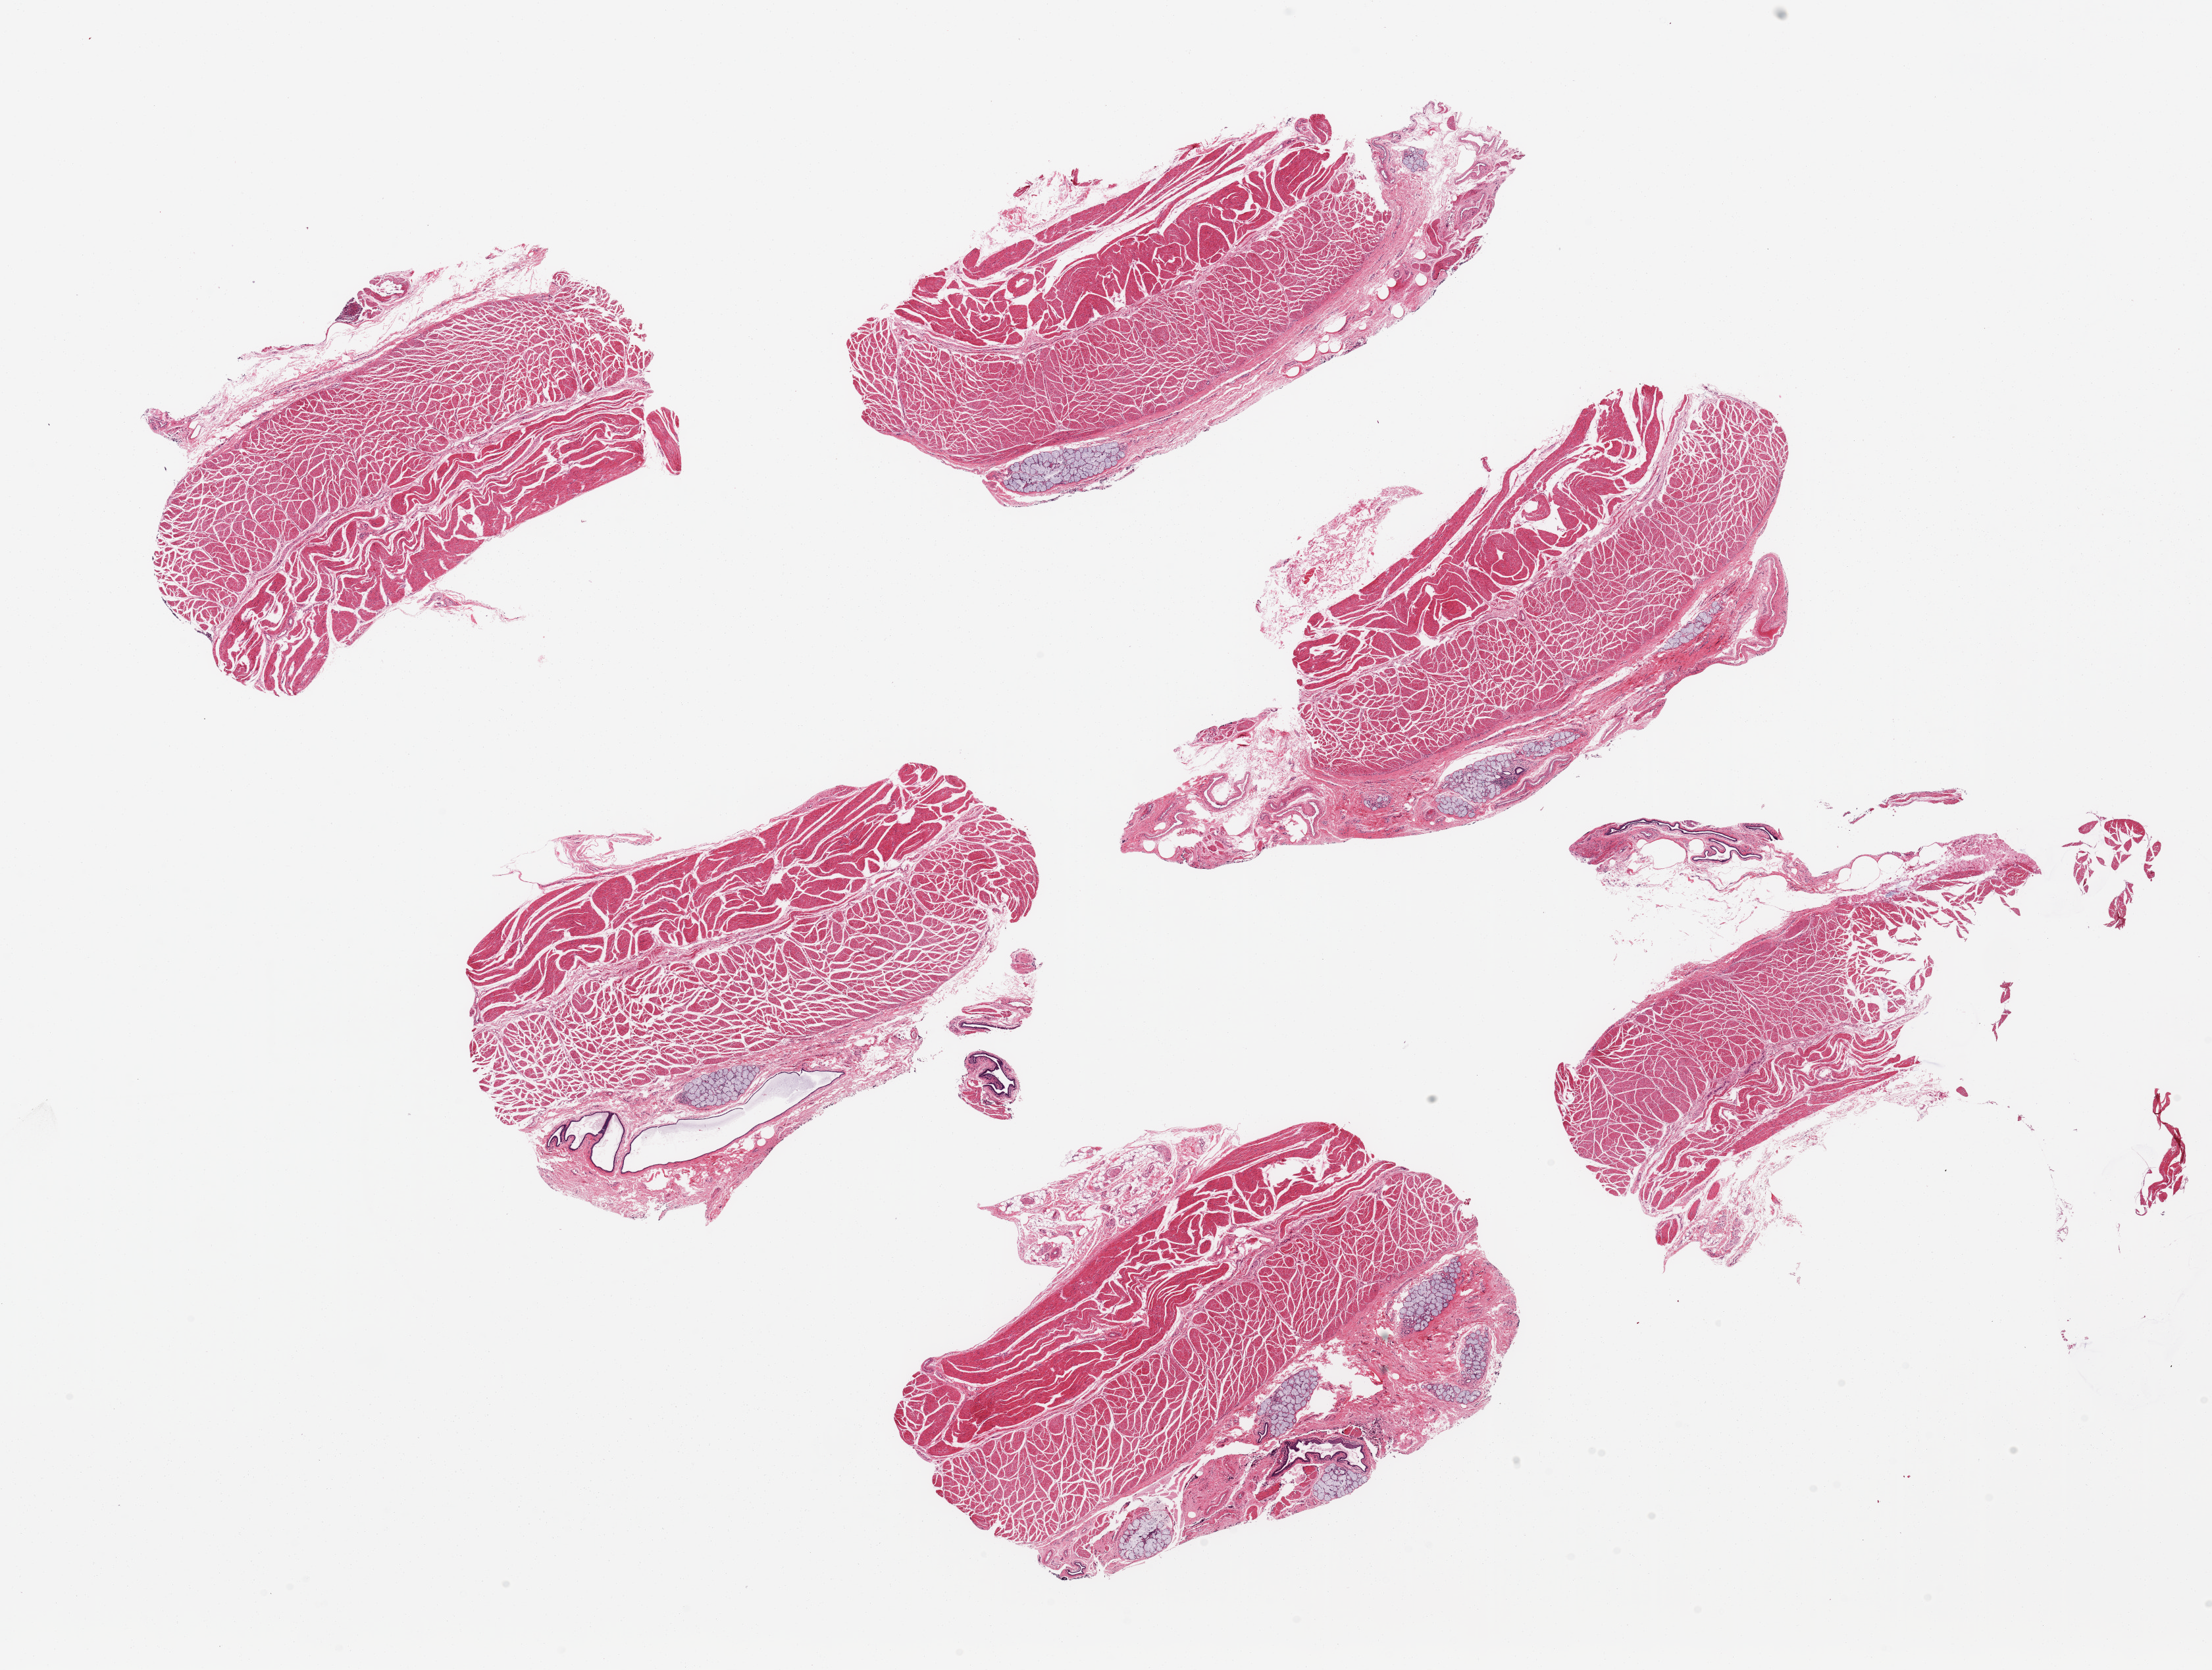
Whole-slide image, haematoxylin and eosin stain — low-resolution overview of the scanned area, about 26.6 x 20.1 mm (slide scanned at 20x); PAXgene-fixed paraffin-embedded (PFPE) section; target tissue: esophageal muscle; tissue donor sample. Donor: male.
• pathologist's review note for this sample: 6 pieces, ~7x3.5 mm; 4 aliquots contain prominent submucosal glands and dilated ducts; ganglion cells well preserved